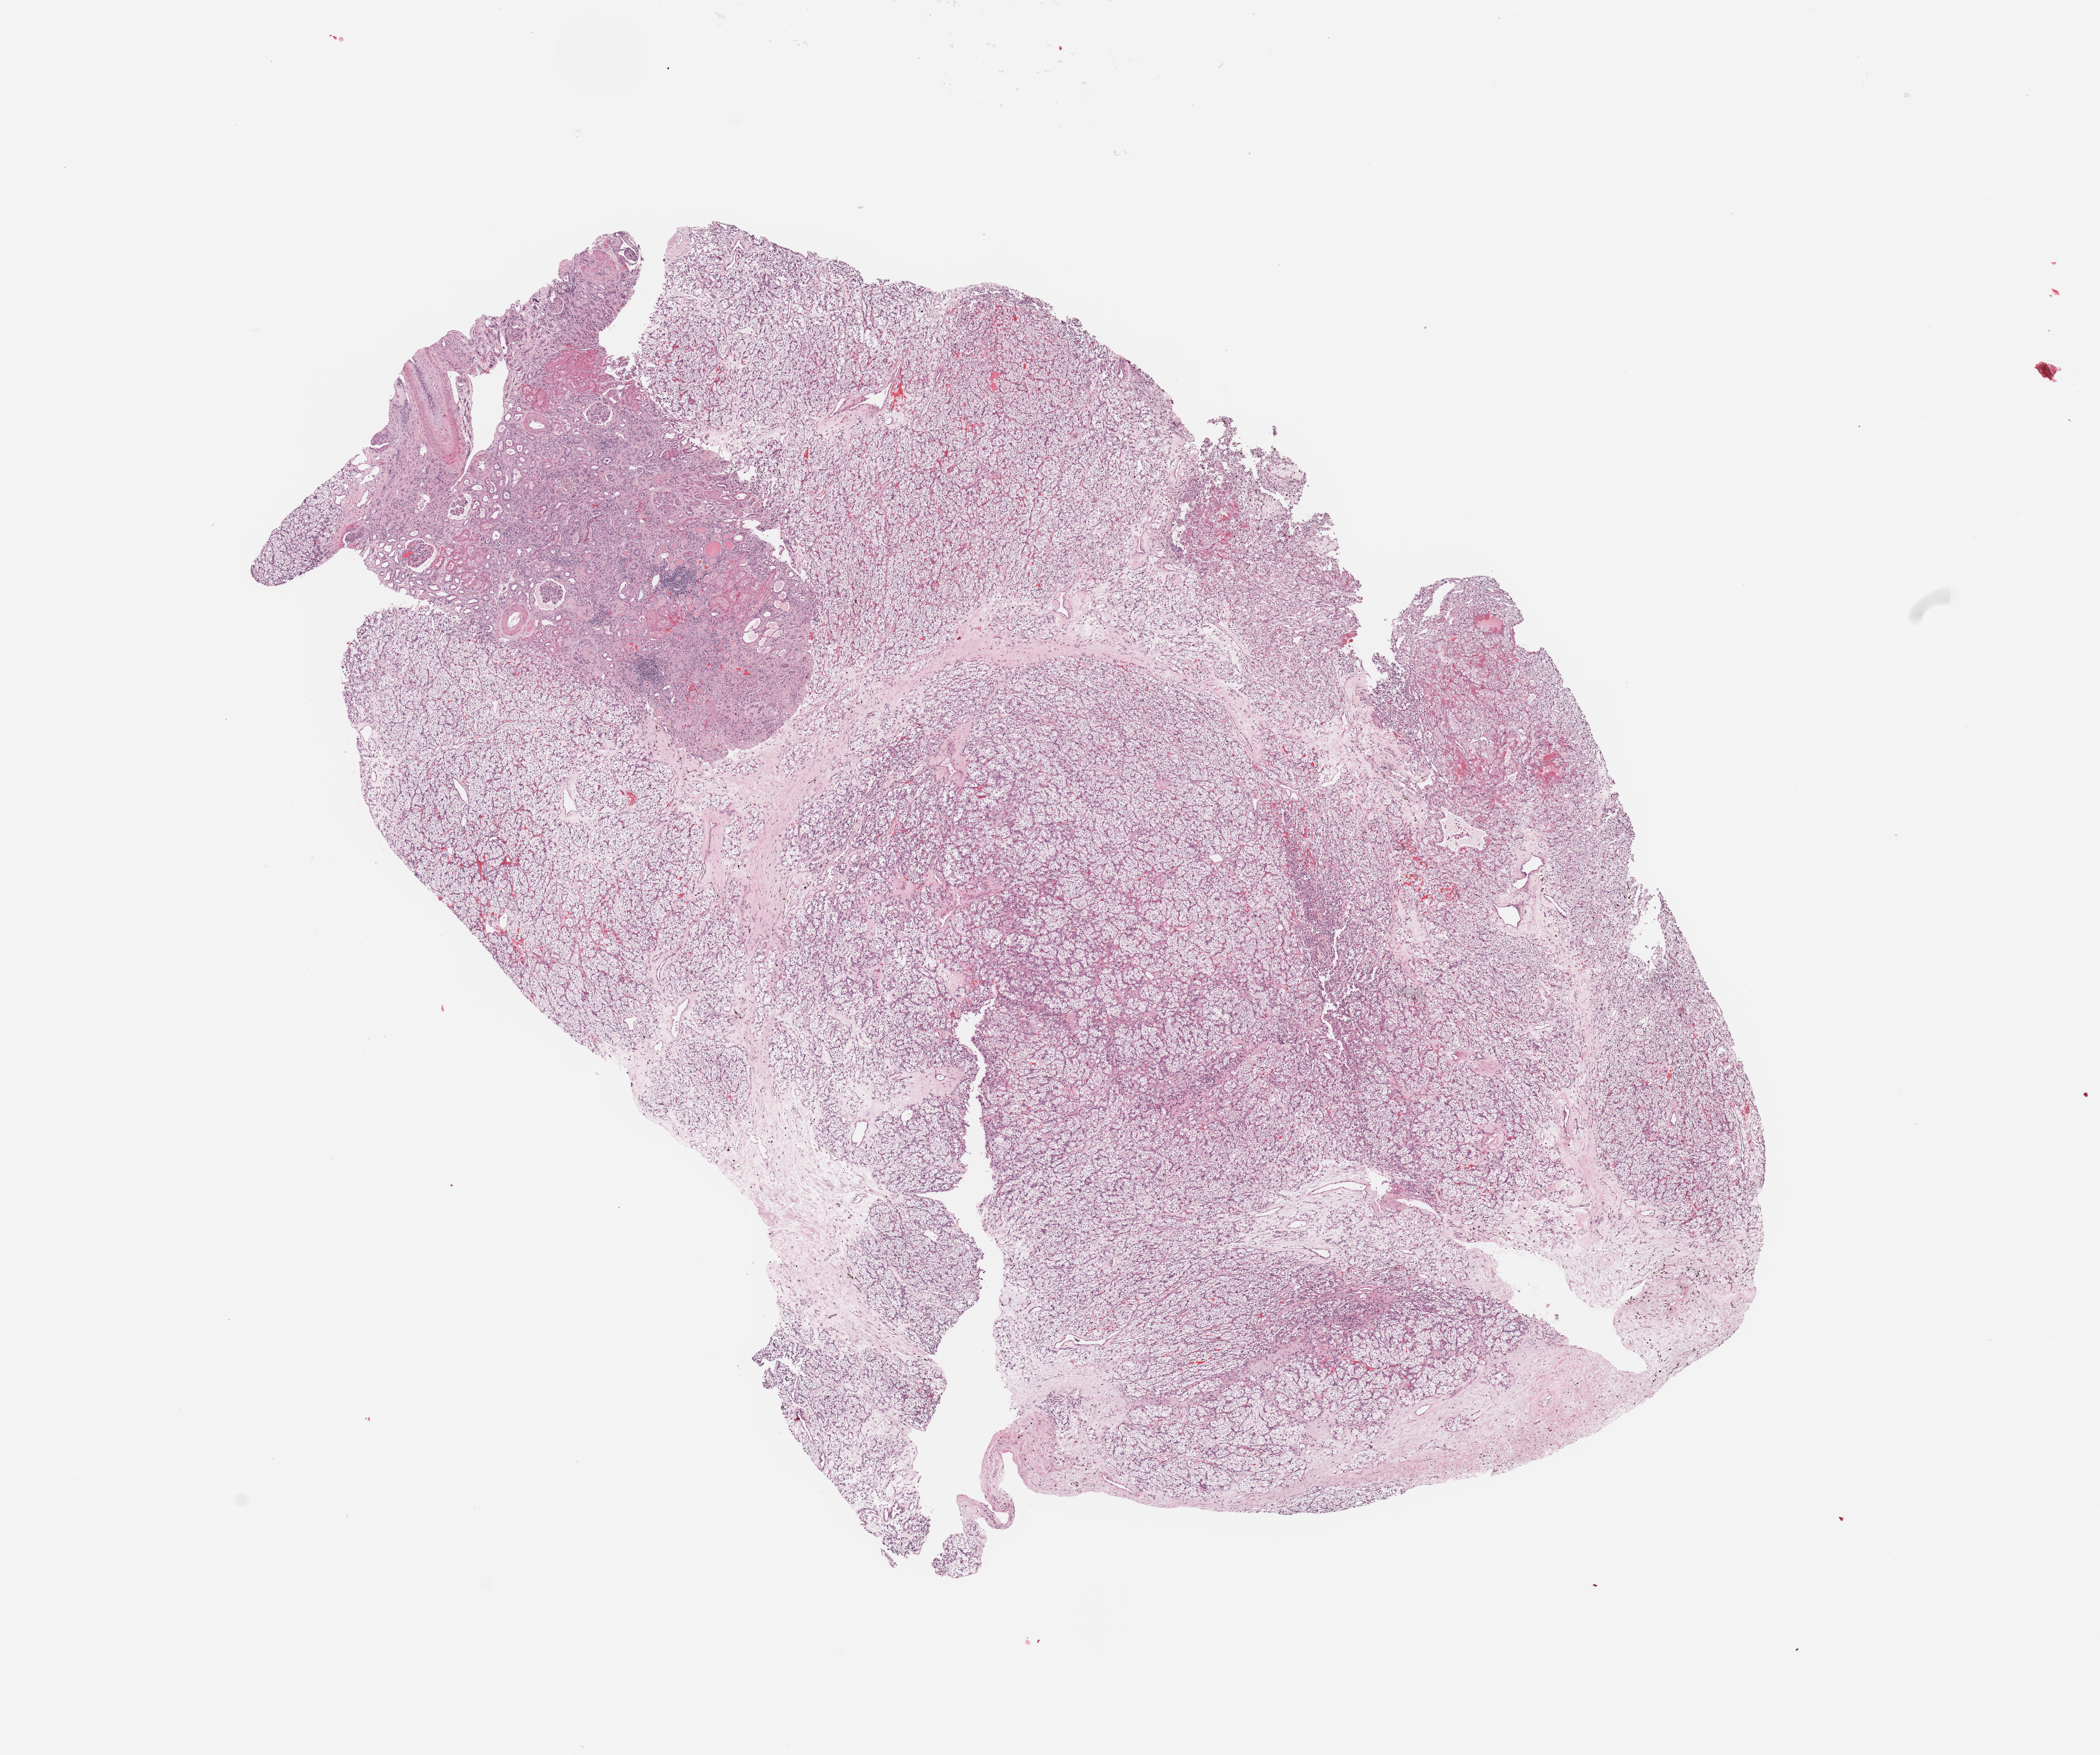
Hematoxylin and eosin (H&E) stained whole-slide image — shown as a low-resolution overview of the whole scanned area (about 13.8 x 11.5 mm, from a 20x scan), tumour tissue sample, sampled site: kidney. 74-year-old male patient. Histologic grade: G2 (moderately differentiated). Composition of this section per pathologist review: tumour nuclei 80%, necrosis 0%.
- primary tumour site (as recorded): upper pole
- diagnosis: Renal cell carcinoma, NOS
- AJCC pathologic stage: I